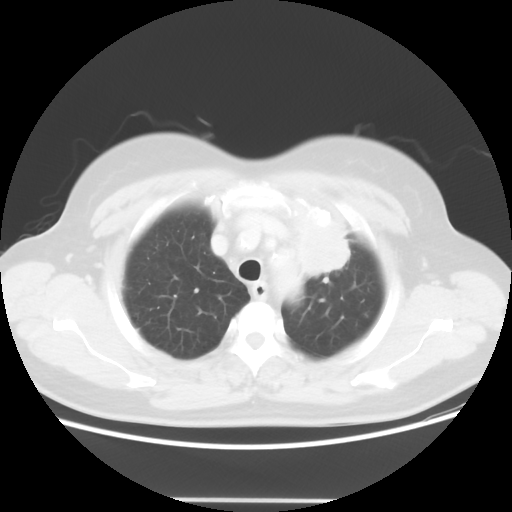
Chest CT, one axial slice. Slice 44 of 52 in the series (ordered by position). Reconstruction kernel STANDARD. Lung window (W 1500 / L -600 HU). 5 mm slice thickness. 512 × 512 image matrix, field of view 382 × 382 mm. Female patient, age 52 years. From the clinical record (not read from this slice): clinical TNM (as recorded): T2 N3 M0.
Structures marked on this image (bounding box drawn by a radiologist):
- lung tumour (recorded histology: adenocarcinoma): bounding box [x1, y1, x2, y2] px = [291, 200, 358, 282]